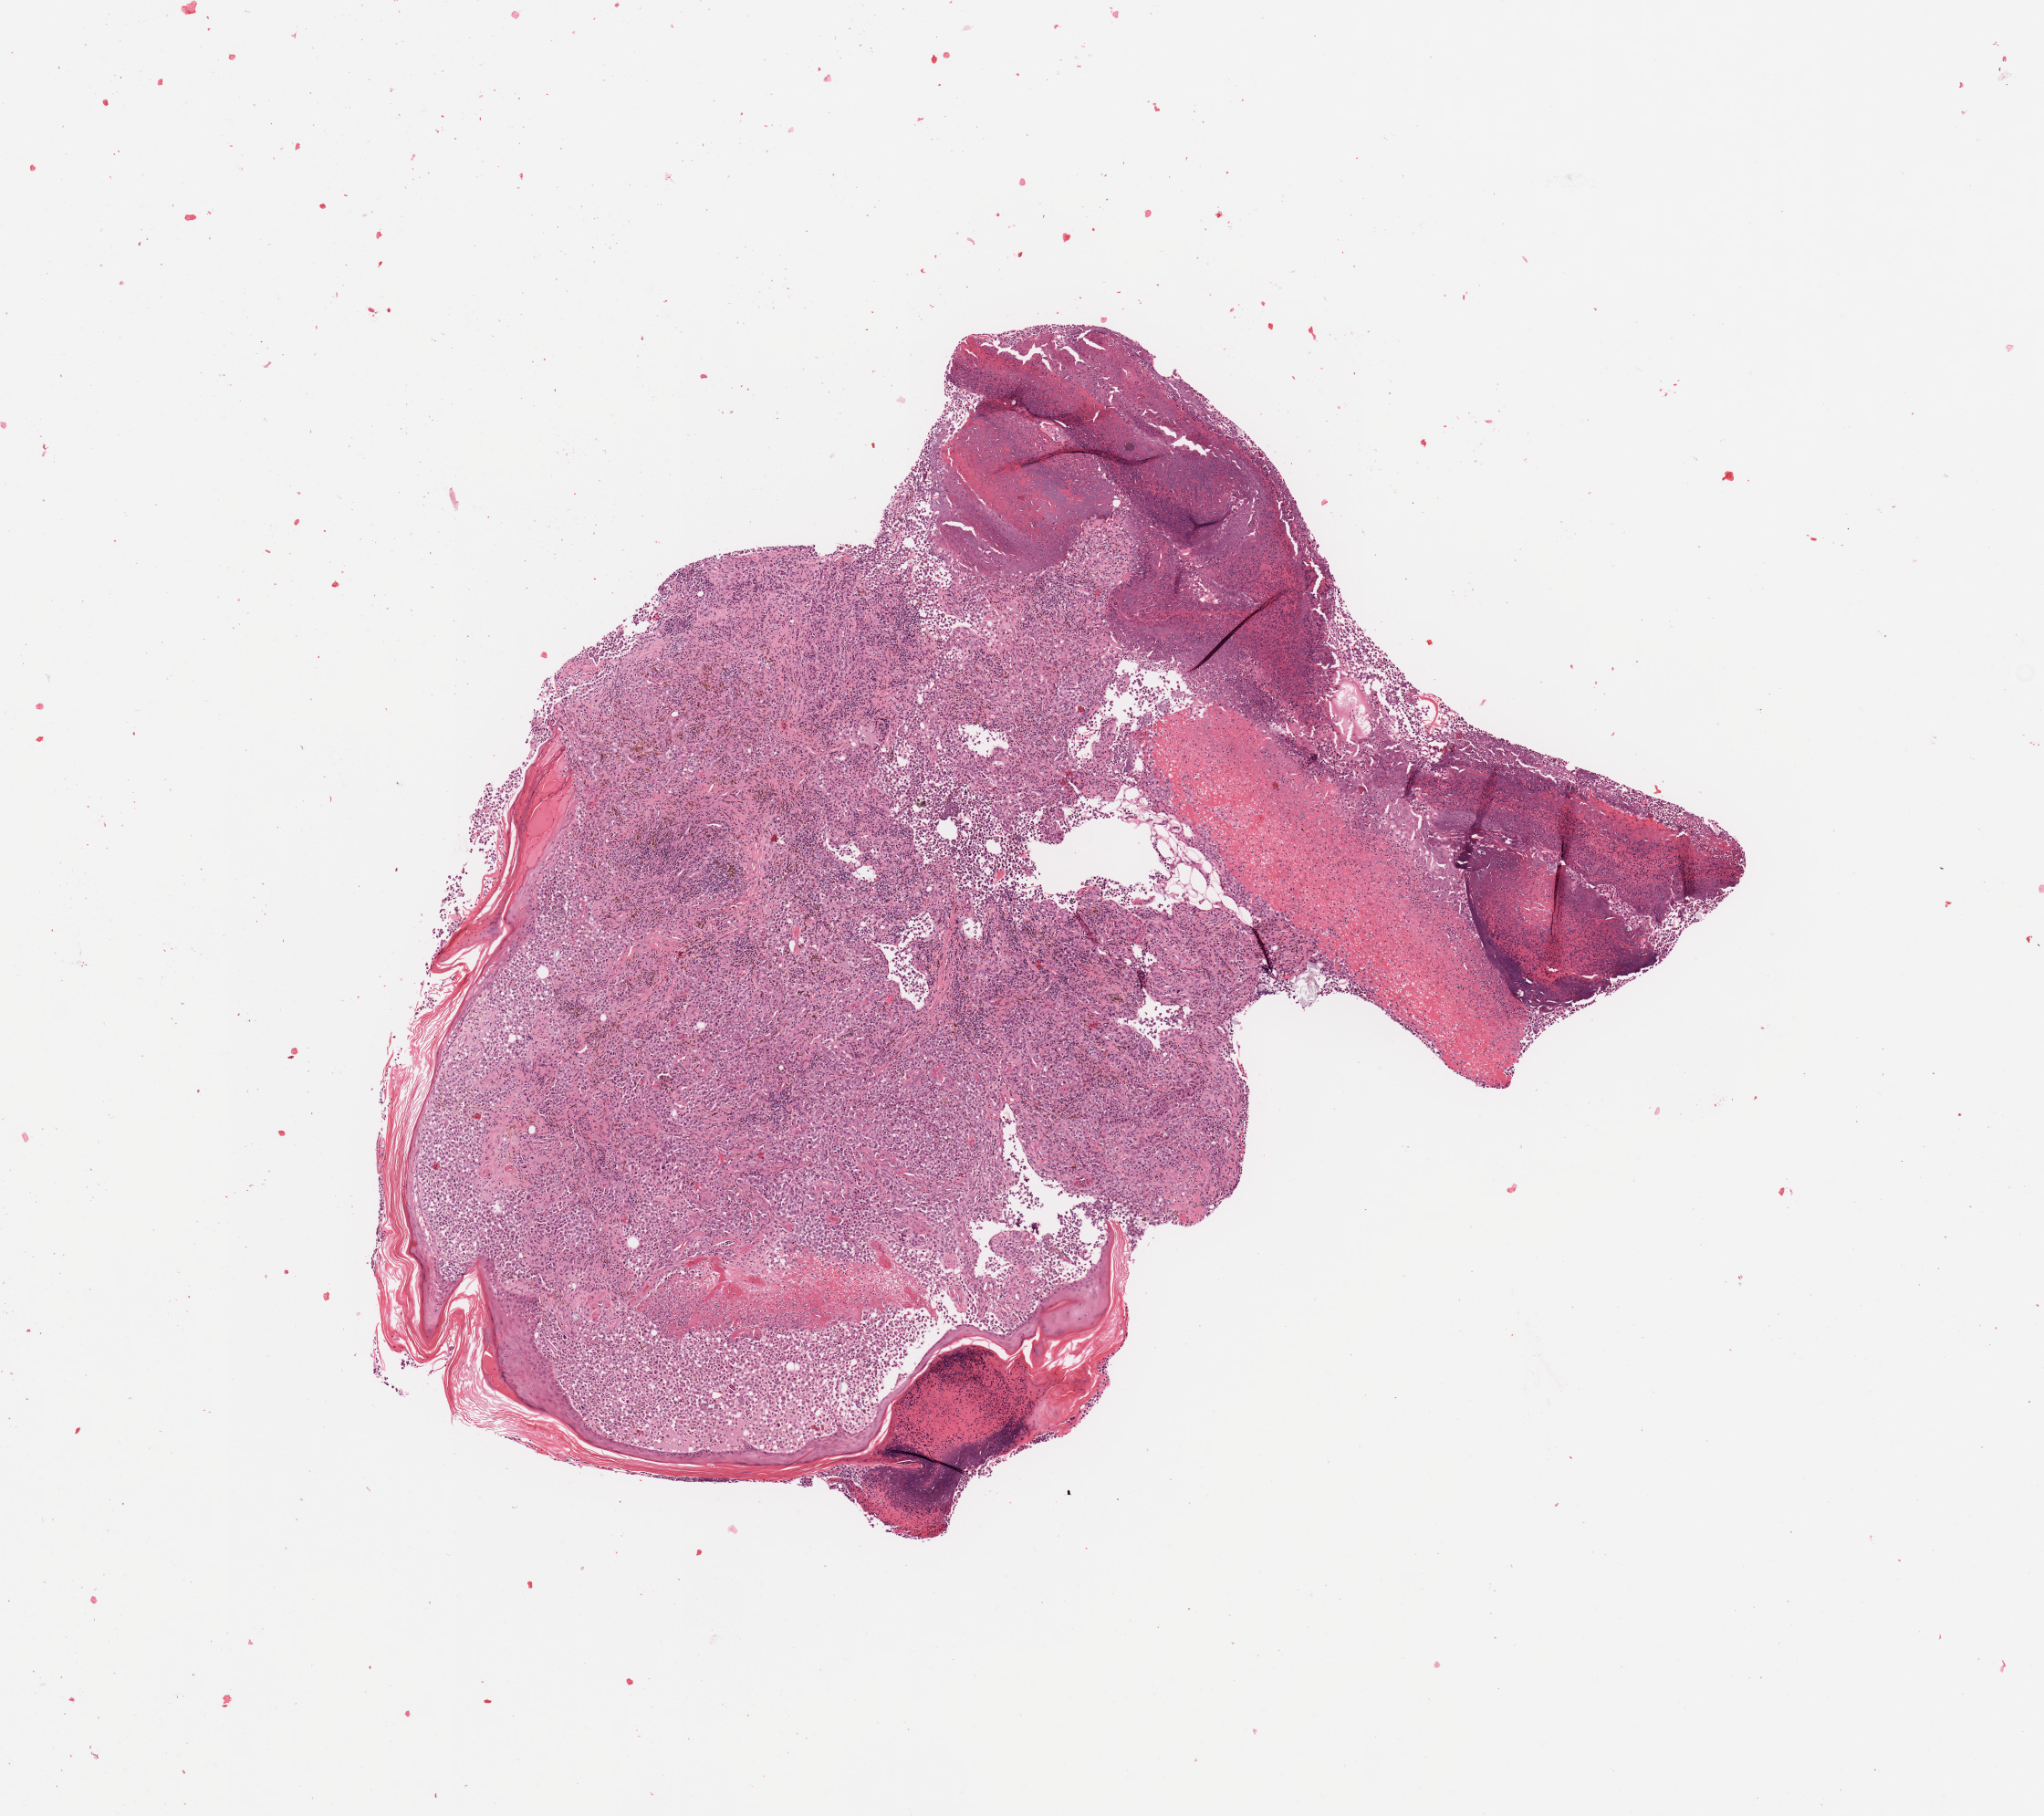
Digitized H&E-stained tissue section (whole slide) — a low-resolution overview of the entire scanned area, about 8.9 x 7.9 mm (from a 20x scan), melanoma tumour tissue; sampled site not recorded. Patient: female, age 64 years.
Diagnosis: Malignant melanoma, NOS. Primary tumour site (as recorded): extremities. AJCC pathologic stage: IIIC.